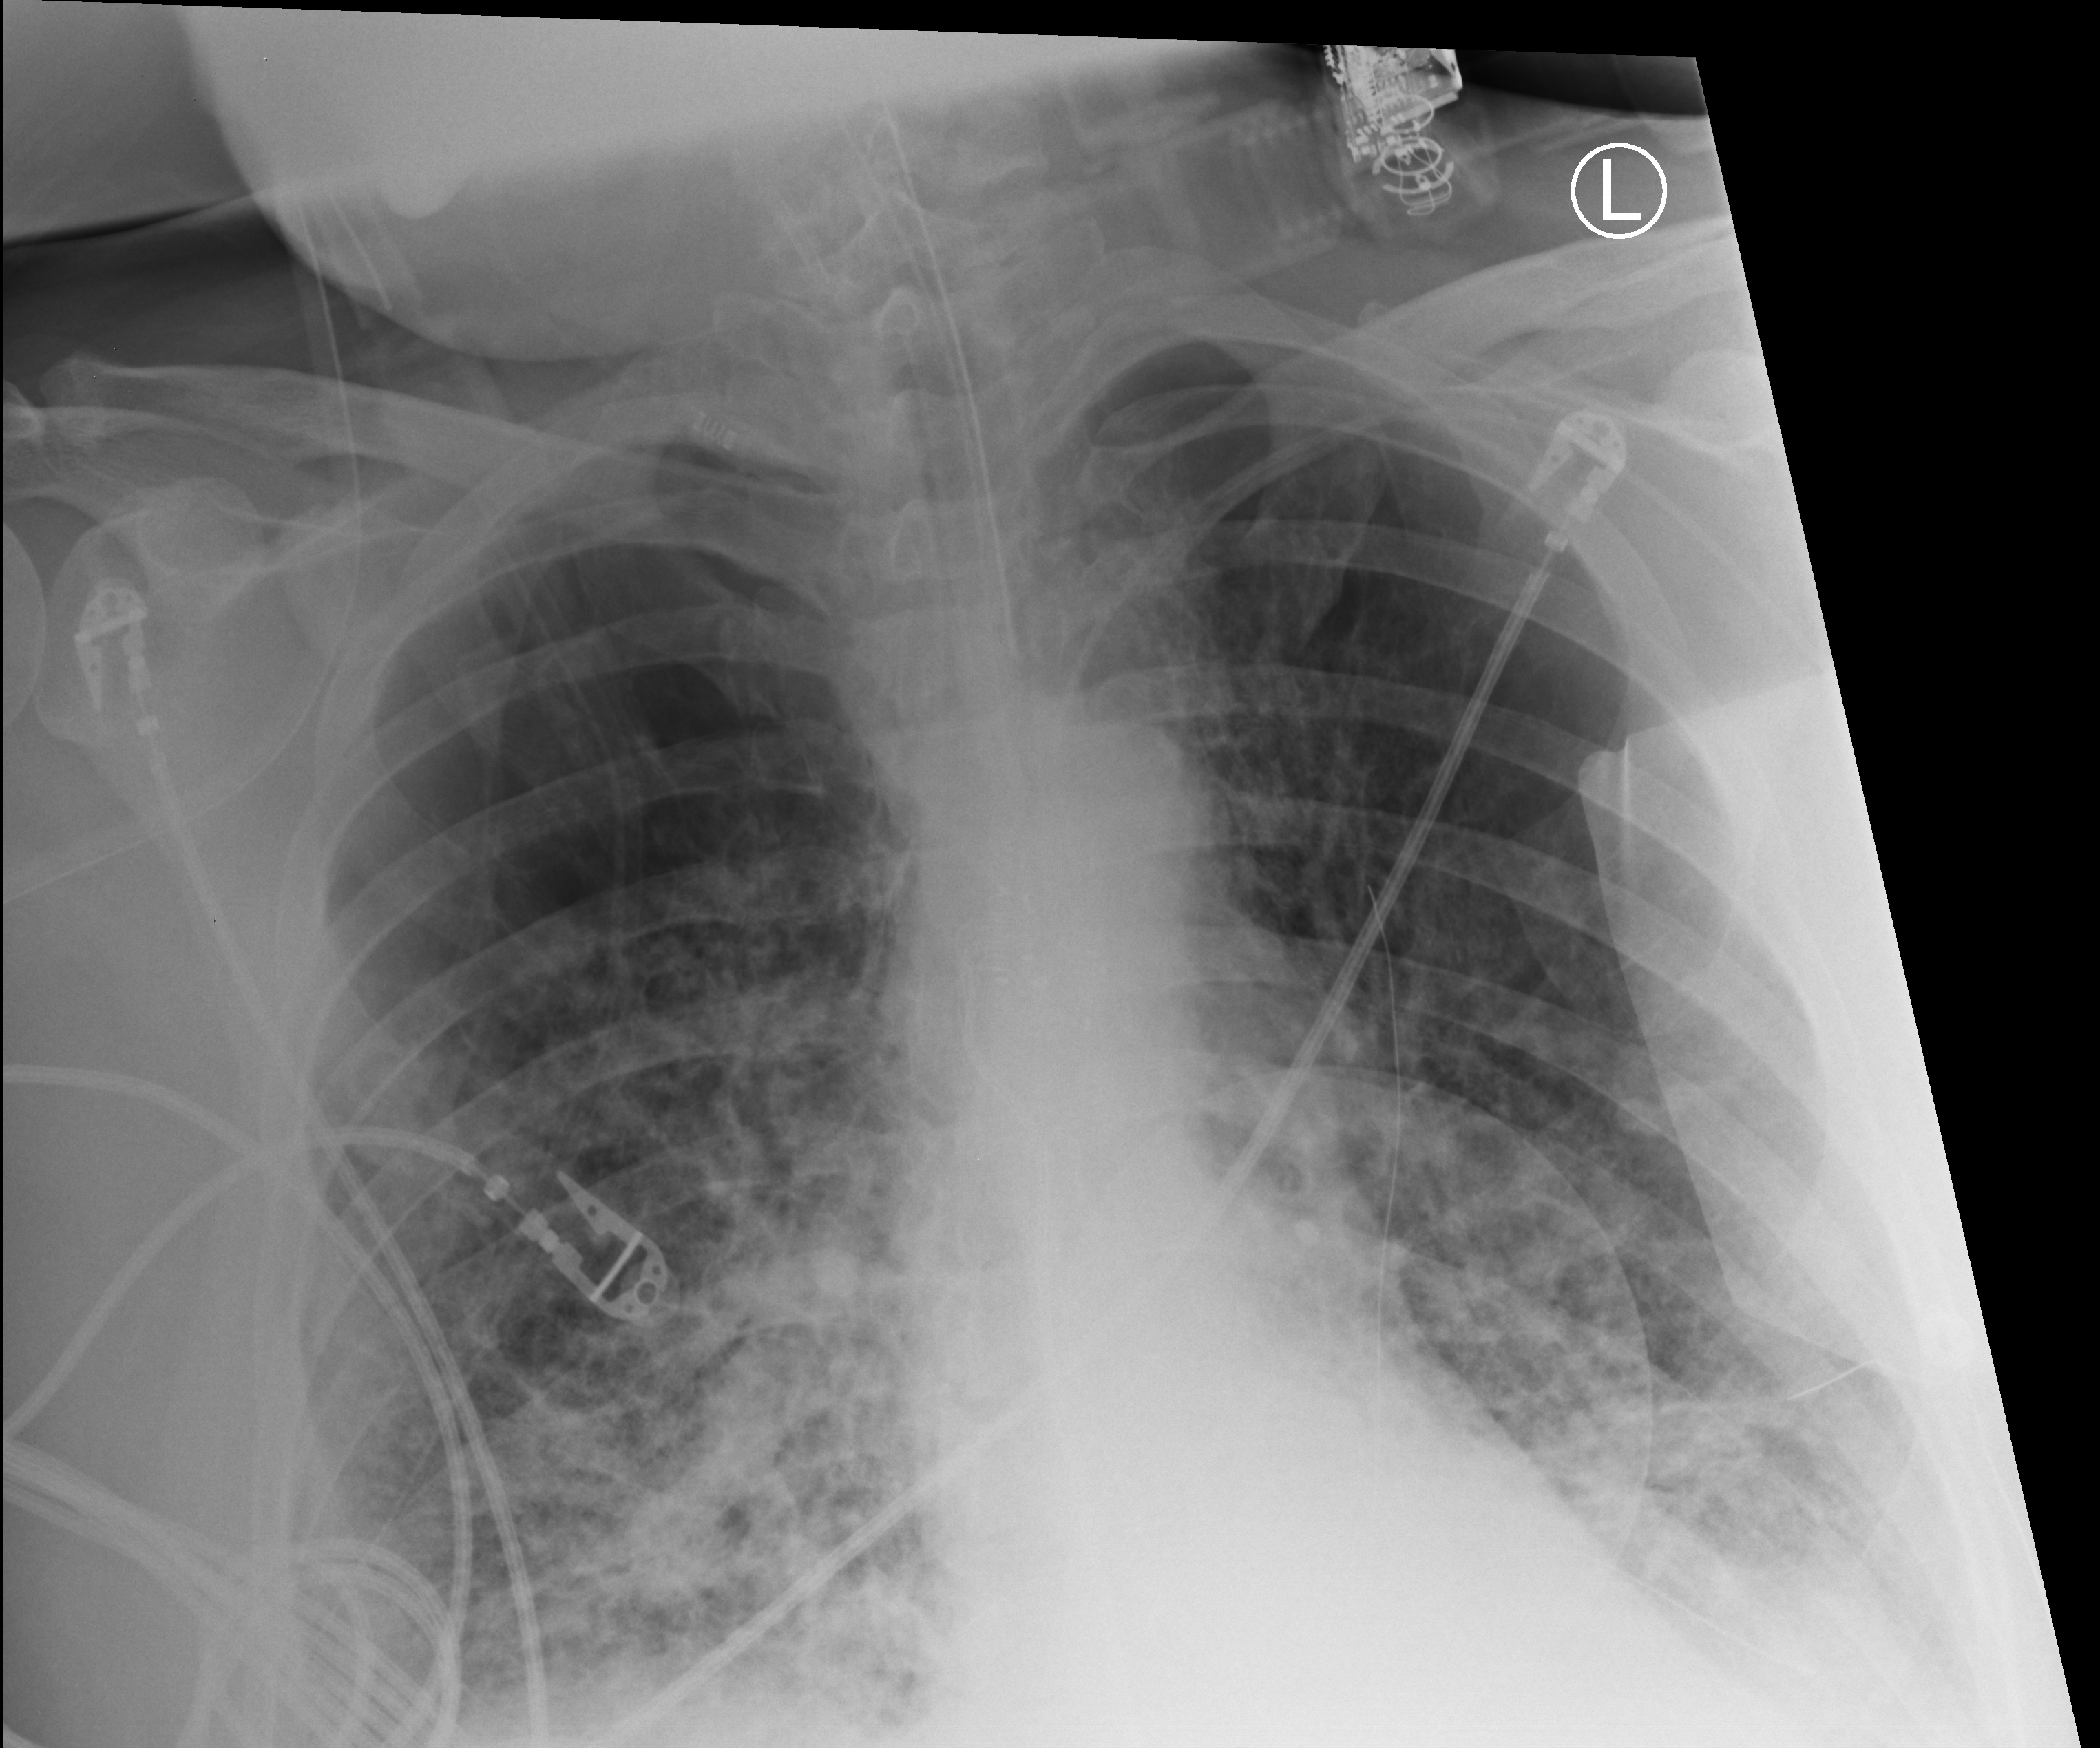
Portable chest radiograph; anteroposterior (AP) projection. Adult patient hospitalised with COVID-19, age 18–59 years.
Hospital-stay facts (about this admission, not read from this image; timing relative to this image not recorded): other chronic lung disease (admission record): yes.